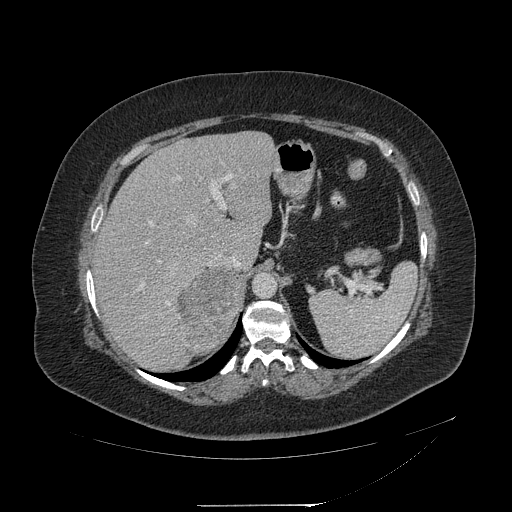
Contrast-enhanced abdominal CT, one axial slice; slice 152 of 217 in the series (ordered by position); soft-tissue window (W 400 / L 40 HU); 512 × 512 image matrix, field of view 453 × 453 mm. Female patient, age 55 years. Case-level facts recorded for this patient, not image findings: diagnosis: adrenocortical carcinoma; tumour side: right adrenal; tumour size at pathology: 11 cm; Ki-67 index: 20 %; stage (as recorded): 2.
Annotated regions visible in this slice (semi-automatically segmented with operator editing):
- mass: bounding box <178,267,242,351> (left, top, right, bottom; pixels)